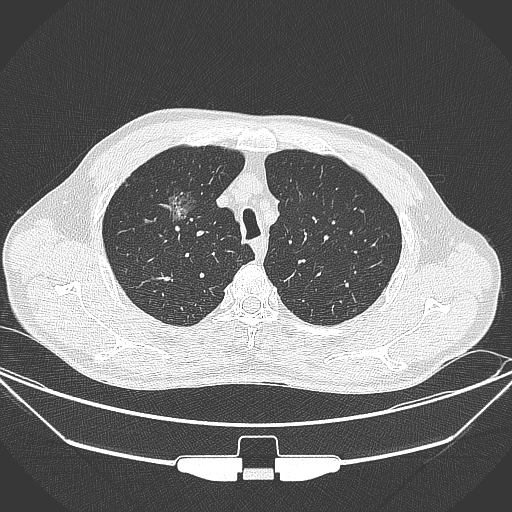
Chest CT, one axial slice; position 275 of 355 along the scan axis; 120 kVp; lung window (W 1500 / L -600 HU); 1 mm slice thickness; 512 × 512 image matrix, field of view 399 × 399 mm. Male patient, age 67 years. Case-level facts recorded for this patient, not image findings: clinical TNM (as recorded): T1c N0 M0.
Structures marked on this image (rectangle marked by the reading radiologist):
- lung tumour (recorded histology: adenocarcinoma): bounding box [x1, y1, x2, y2] px = [156, 184, 205, 236]